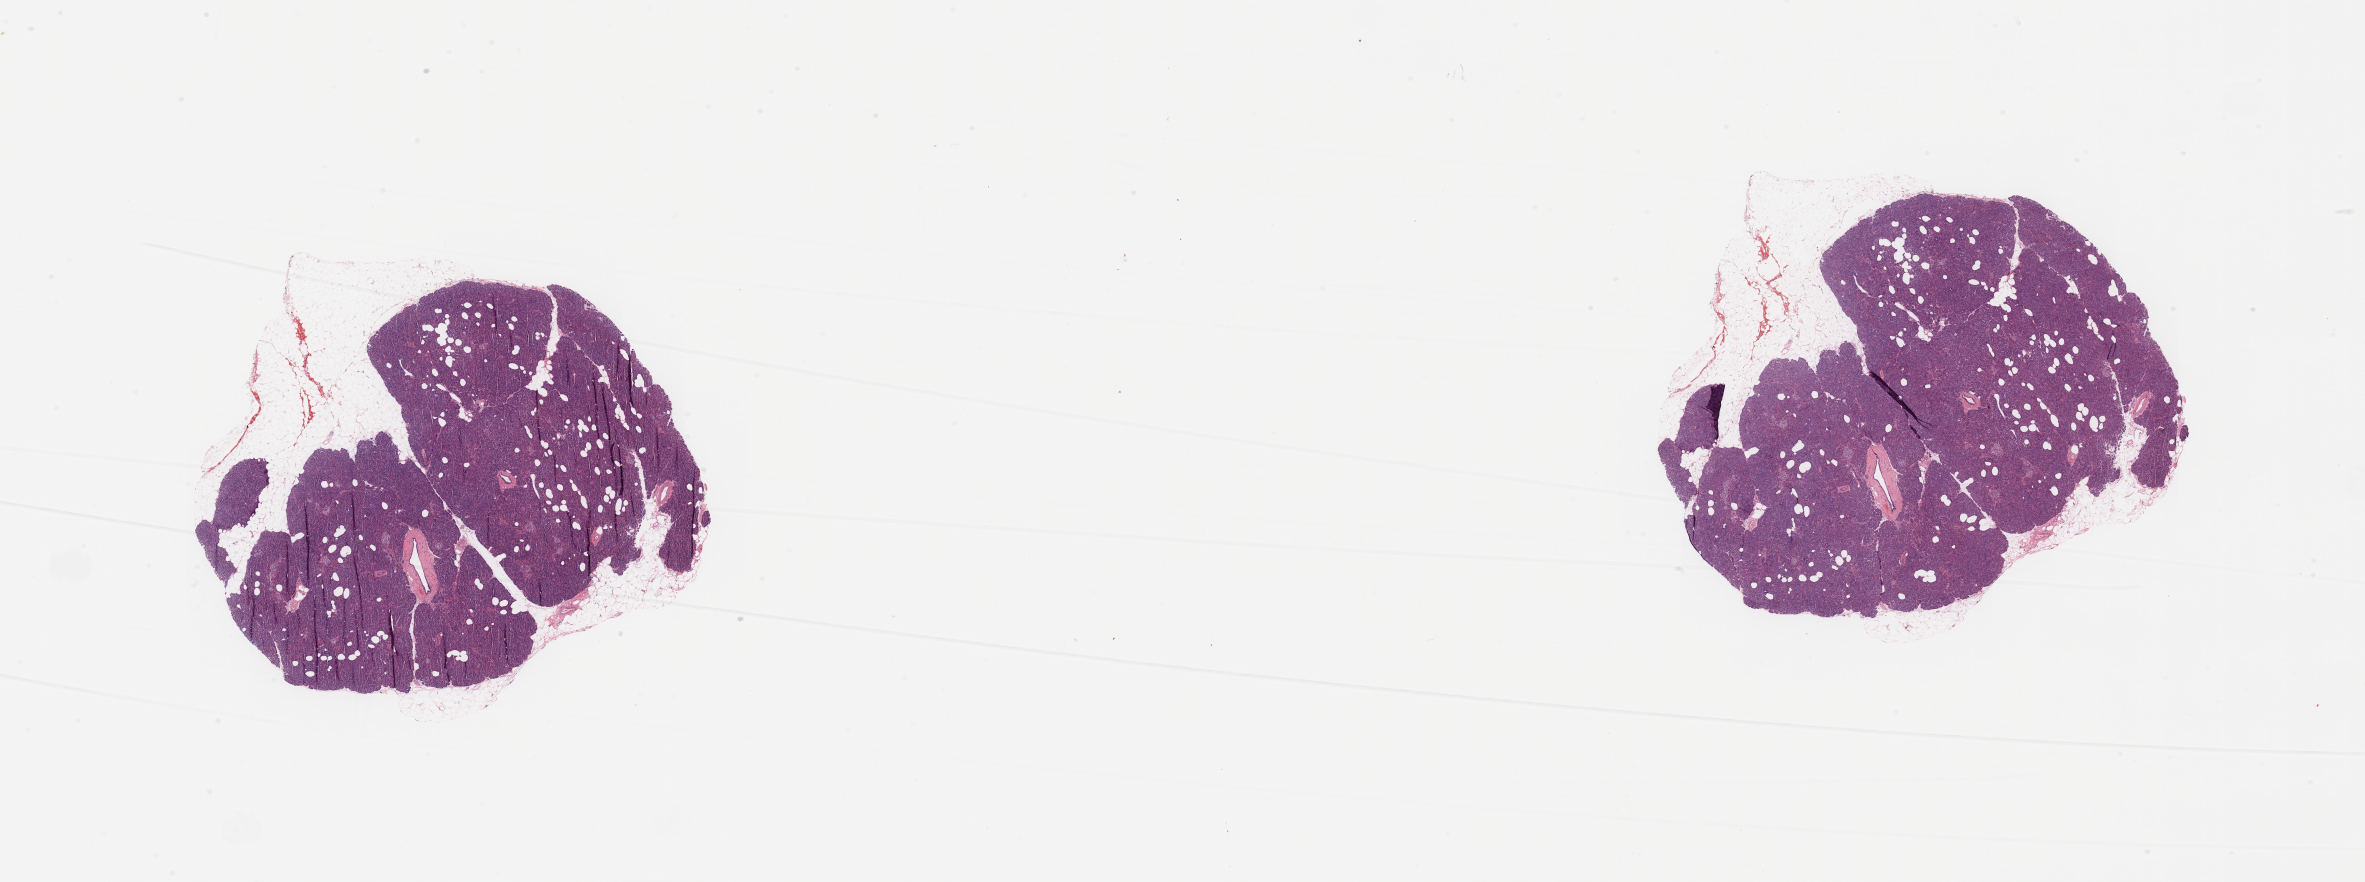
Whole-slide histology image, Hematoxylin and eosin (H&E) stained — a low-resolution overview of the entire scanned area, about 37.4 x 14.0 mm (acquisition: 20x scan); normal (non-tumour) tissue sample, sampled site: pancreas. Male, 66 y/o.
This section: normal (non-tumour) tissue from the same patient. Patient diagnosis: Infiltrating duct carcinoma, NOS.